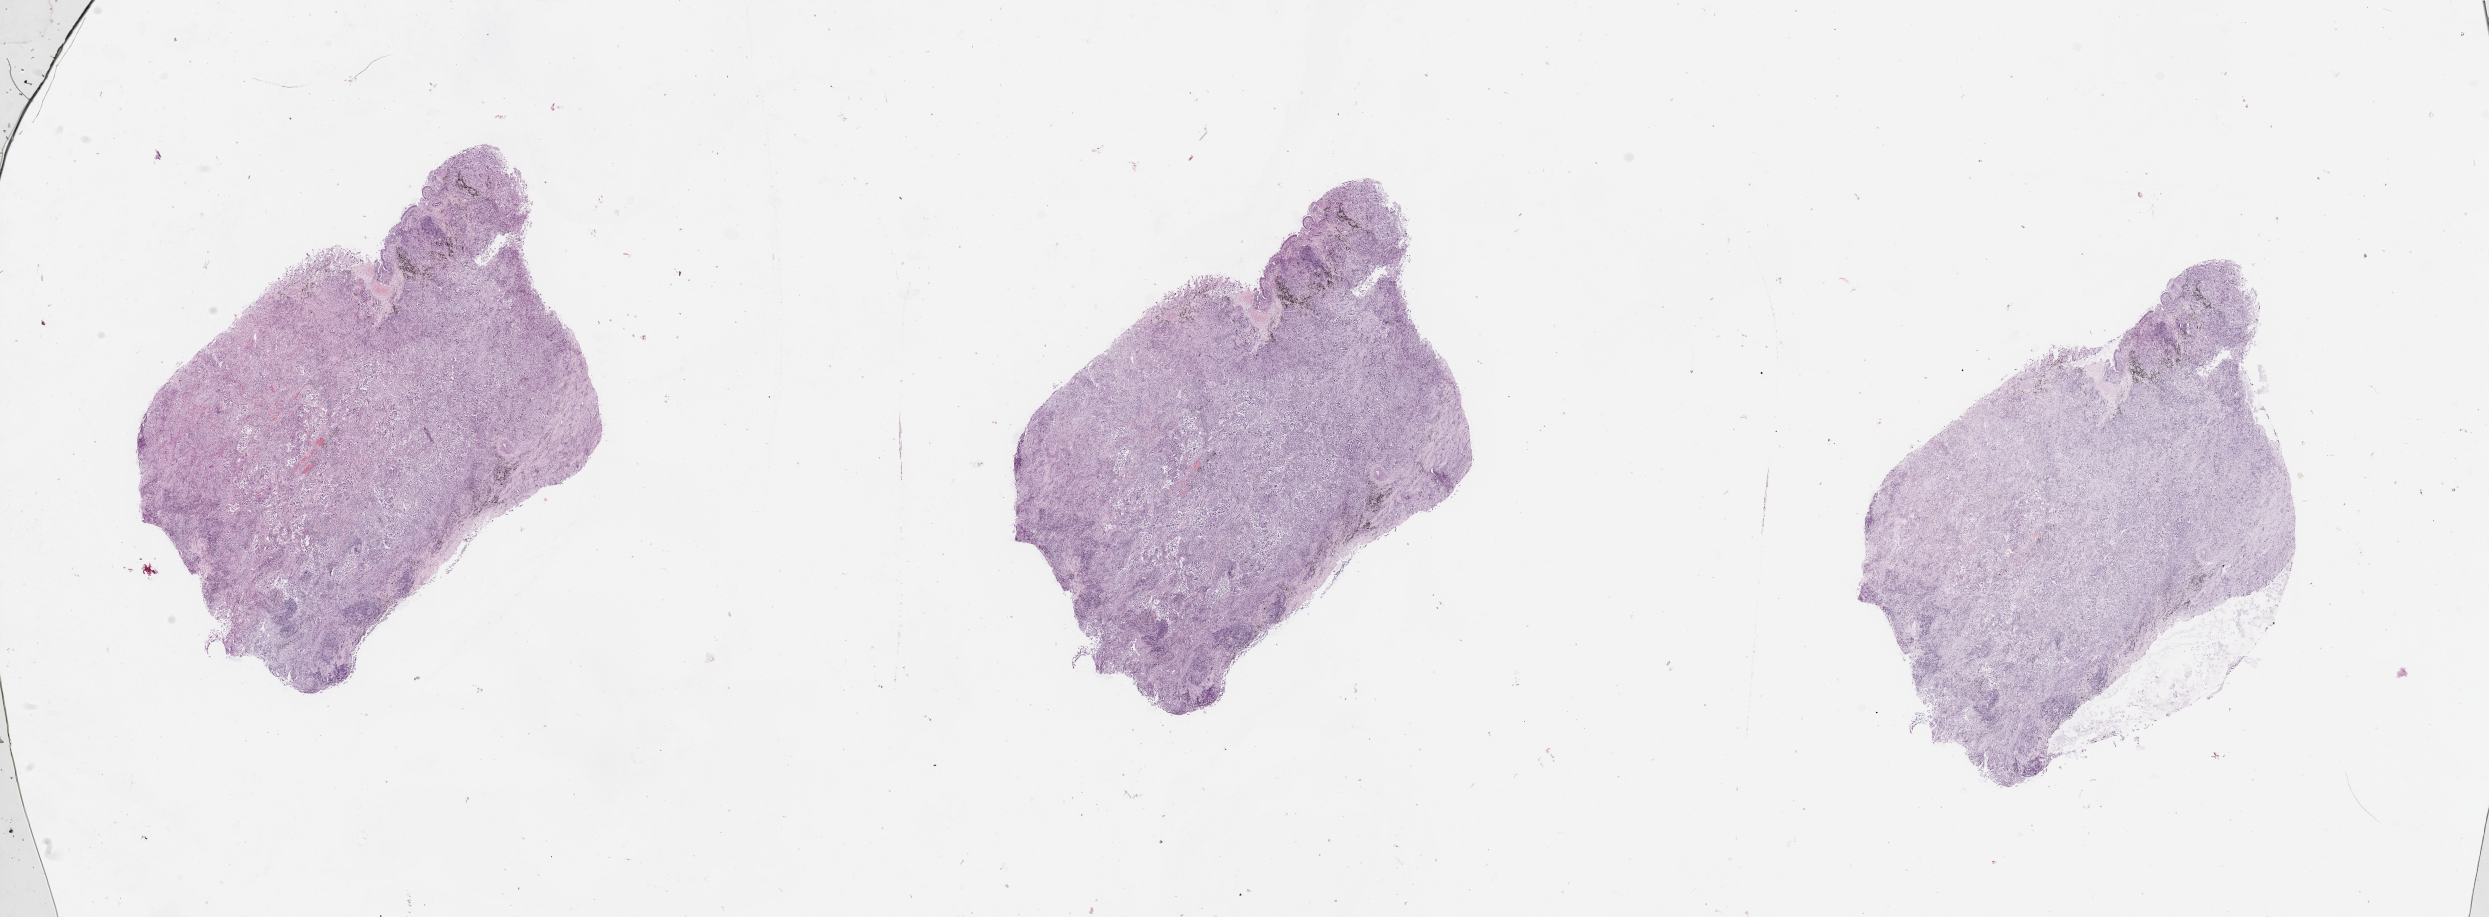
Hematoxylin and eosin (H&E) stained whole-slide image — whole scanned area (about 39.4 x 14.5 mm, slide scanned at 20x) shown as a low-resolution overview. Tumour tissue sample, sampled site: lung. Patient: male, age 76 years. Histologic grade: G2 (moderately differentiated). Composition of this section per pathologist review: tumour nuclei 75%, necrosis 5%.
AJCC pathologic stage: IIA. Histologic diagnosis: Adenocarcinoma, NOS.